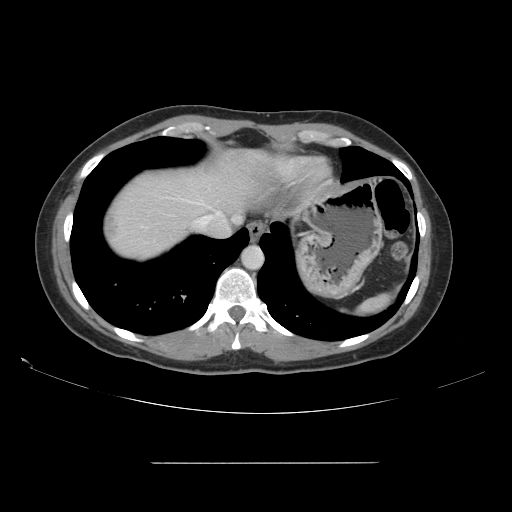
Contrast-enhanced abdominal CT, one axial slice; slice 136 of 151 in the series (ordered by position); 120 kVp; soft-tissue window (W 400 / L 40 HU); 2.5 mm slice thickness; 512 × 512 image matrix, field of view 421 × 421 mm. Female patient, age 46 years. From the clinical record (not read from this slice): diagnosis: colorectal cancer liver metastases, imaged before liver resection; multiple liver metastases: yes; largest metastasis: 3 cm.
Annotated regions visible in this slice (outlined manually by an expert reader):
- hepatic veins: bounding box [x1, y1, x2, y2] px = [197, 212, 221, 227]
- liver: [102, 152, 248, 259]
- planned liver remnant (the part of the liver to remain after resection): [116, 165, 248, 231]
- liver metastasis: [108, 214, 117, 232]